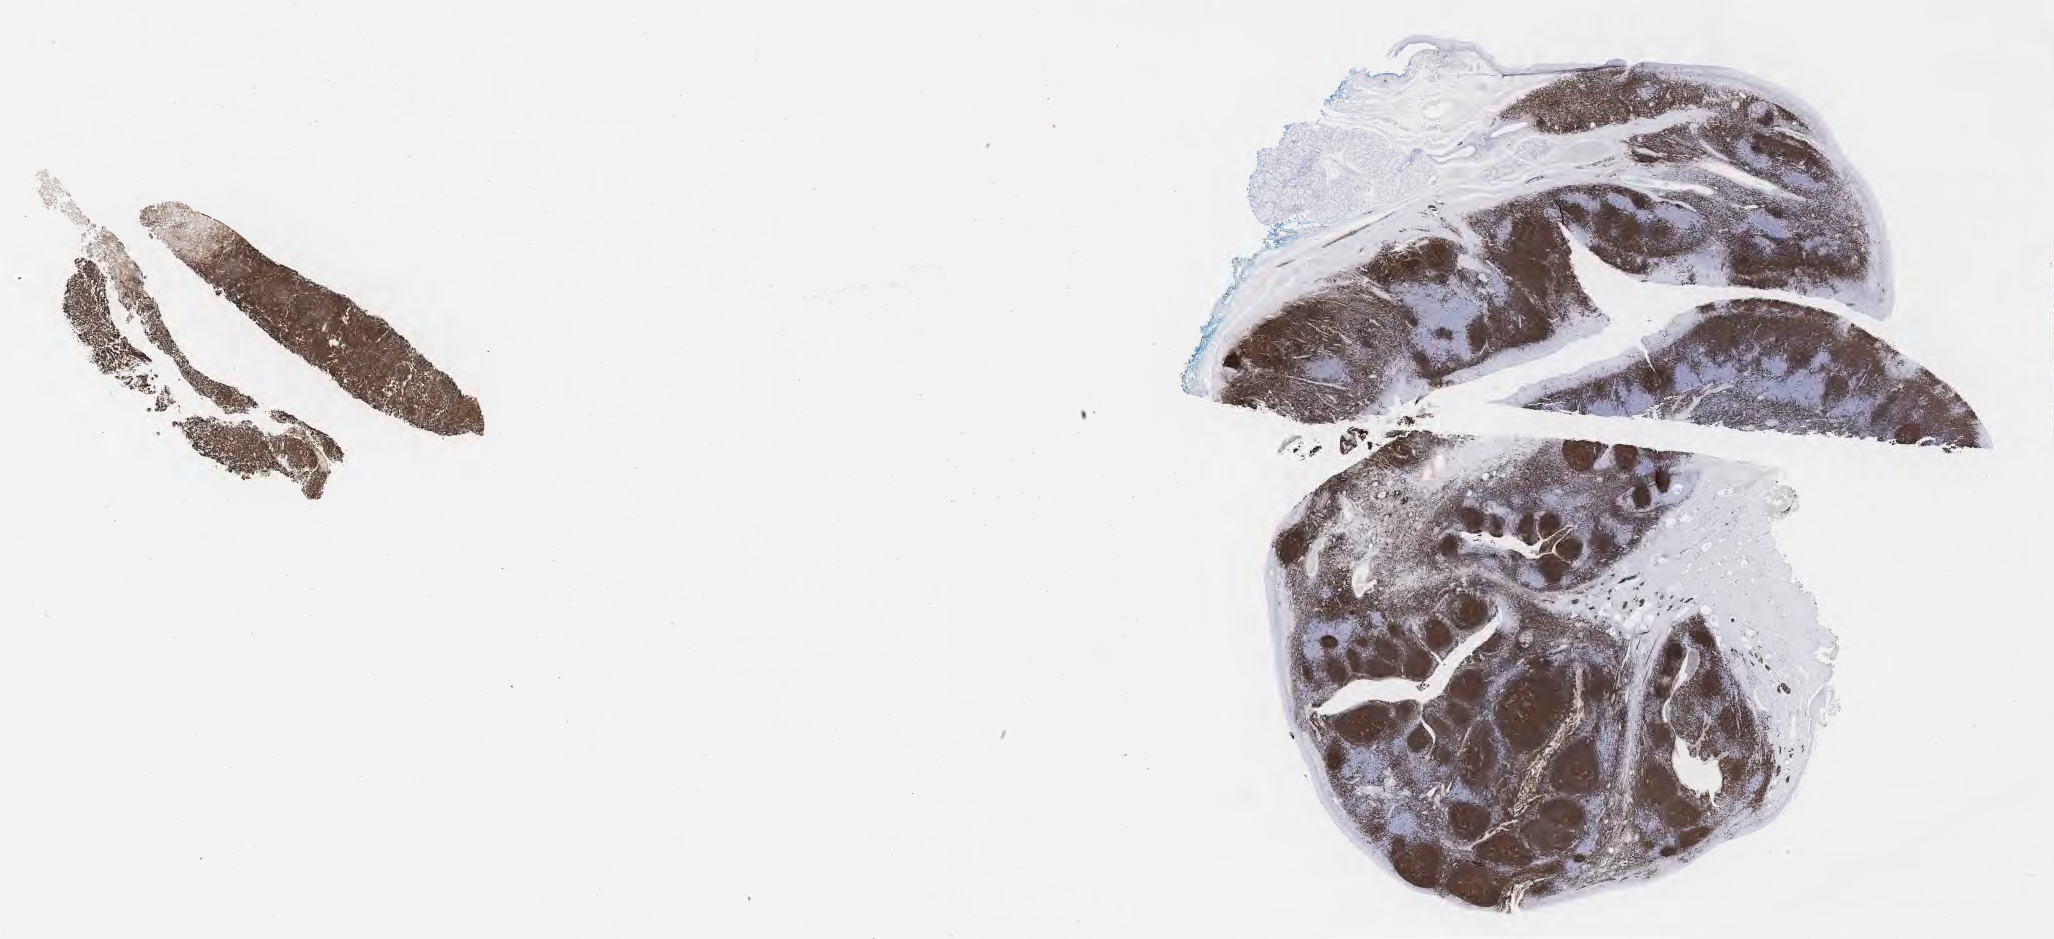
Whole-slide image, immunohistochemical stain for CD20 — a low-resolution overview of the entire scanned area, about 33.2 x 15.2 mm. Specimen: tumor tissue. Patient female; aged 18.
Histologic diagnosis: Burkitt lymphoma, NOS.